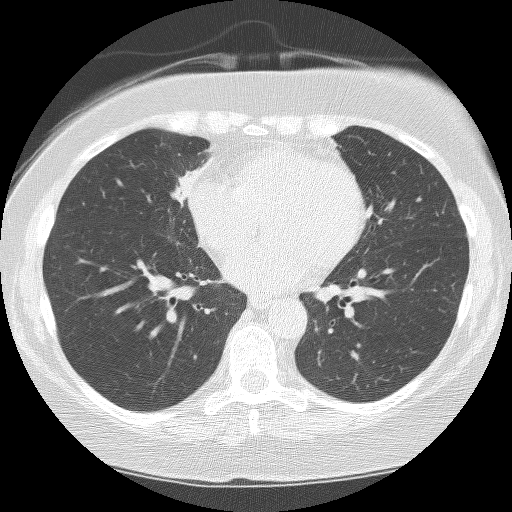
Low-dose screening chest CT, one axial slice. Position 77 of 159 along the scan axis. 120 kVp. Lung window (W 1500 / L -600 HU). 512 × 512 image matrix.
Annotated regions visible in this slice (manually delineated by an expert):
- lesion 1 (tumor, hilum of right lung): bounding box [x1, y1, x2, y2] px = [170, 160, 214, 207]